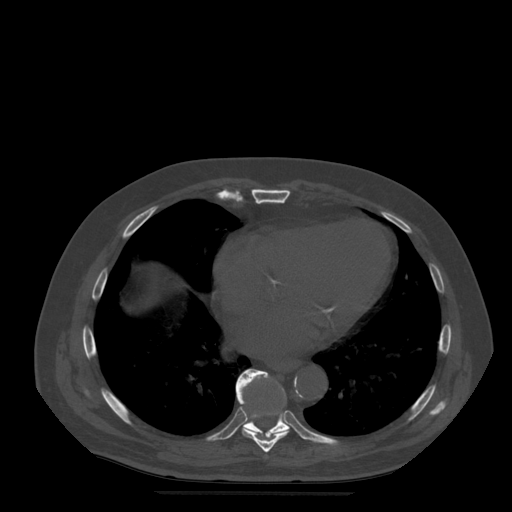
CT including the spine, one axial slice. Slice 303 of 522 in the series (ordered by position). Bone window (W 1800 / L 400 HU). 512 × 512 image matrix, field of view 420 × 420 mm. Patient age 72 years. Case-level facts recorded for this patient, not image findings: primary cancer: prostate.
Annotated regions visible in this slice (semi-automatically segmented with operator editing):
- T8 vertebra: bounding box <236,371,290,453> (left, top, right, bottom; pixels)
- T9 vertebra: <236,369,290,437>